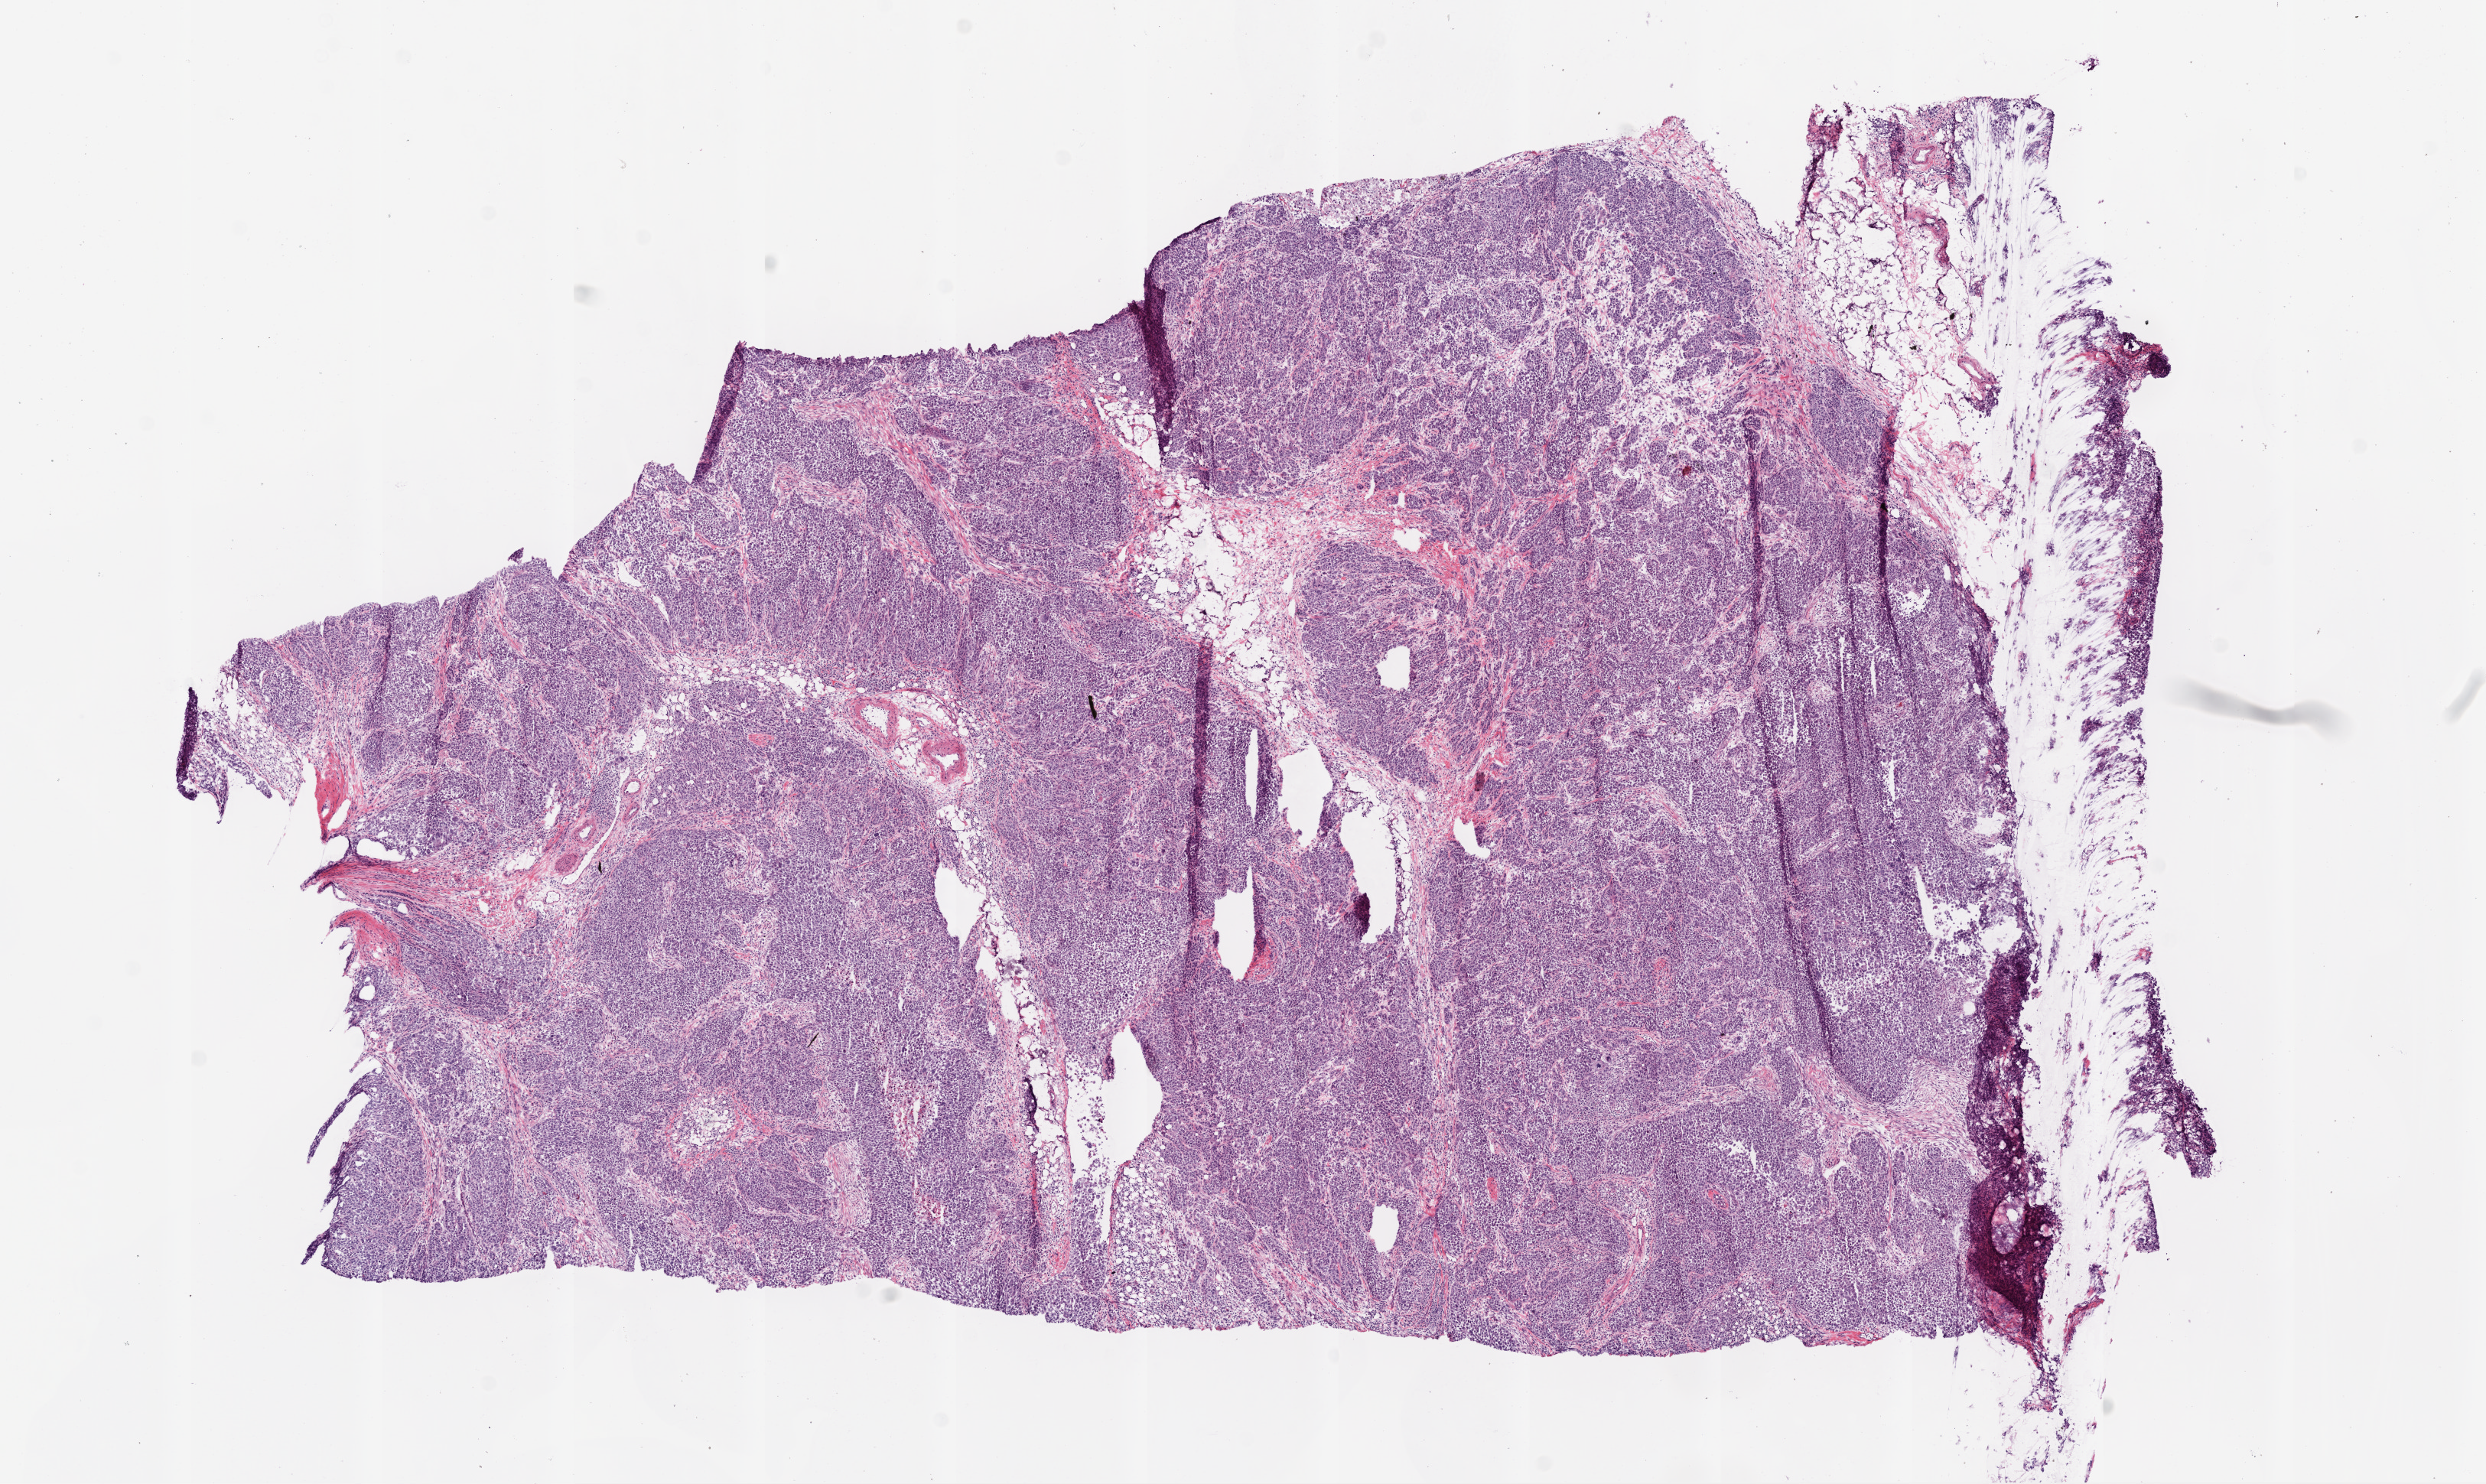
Hematoxylin and eosin (H&E) stained whole-slide image, a low-resolution overview of the entire scanned area, about 13.0 x 7.8 mm (from a 20x scan). Frozen section from the bottom of the tissue portion. Primary tumour sample from the ovary. Female, age 85 years at initial diagnosis. Histologic grade: G3 (poorly differentiated). Pathologist review of this section (percent, as recorded): tumour cells 77%, tumour nuclei 85%, normal cells 10%, stromal cells 8%, necrosis 5%.
- histologic diagnosis: Serous cystadenocarcinoma, NOS
- FIGO stage: IIIC